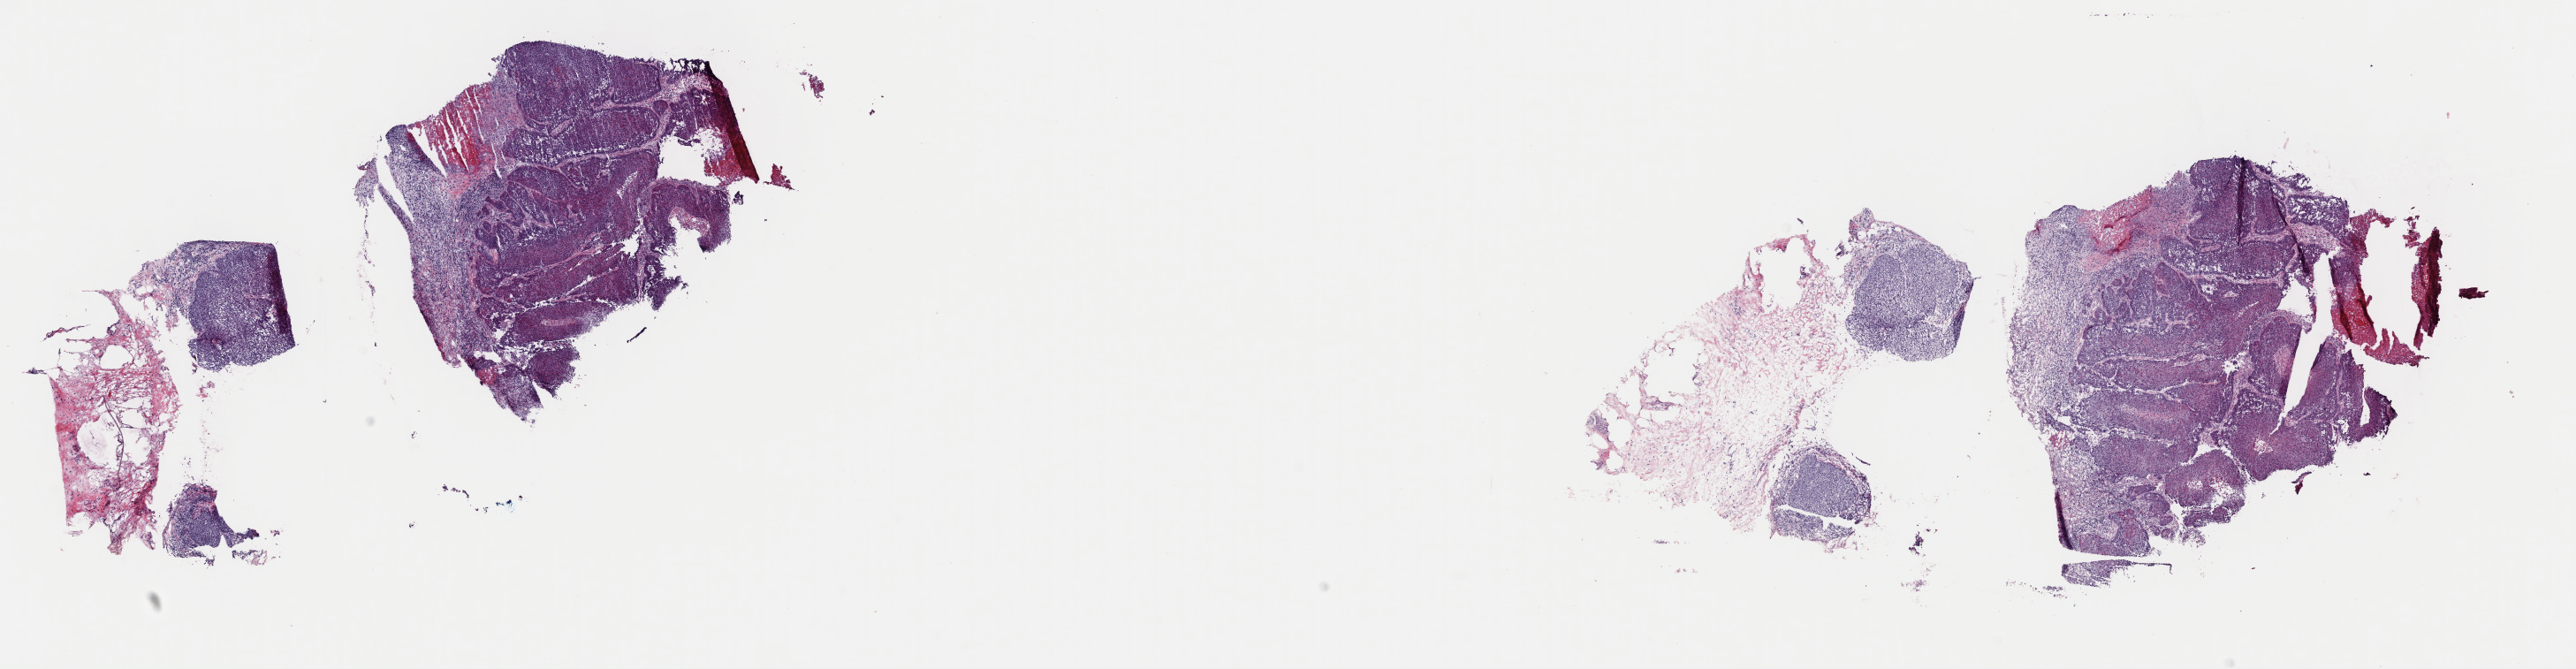
Whole-slide histology image, H&E-stained — shown as a low-resolution overview of the whole scanned area (about 23.0 x 6.0 mm), frozen section from the top of the tissue portion, primary tumour sample from the bladder. Female patient; age at initial diagnosis 80 years. Histologic grade: high grade. Slide review estimates, as recorded: tumour cells 60%, tumour nuclei 70%, normal cells 0%, stromal cells 30%, necrosis 10%. Inflammatory infiltration, as recorded: lymphocyte infiltration 0%, monocyte infiltration 0%, neutrophil infiltration 0%.
- TNM: T3 N0 MX
- pathologic diagnosis: Transitional cell carcinoma
- AJCC pathologic stage: III
- lymph nodes positive (case pathology): 0 of 2 examined